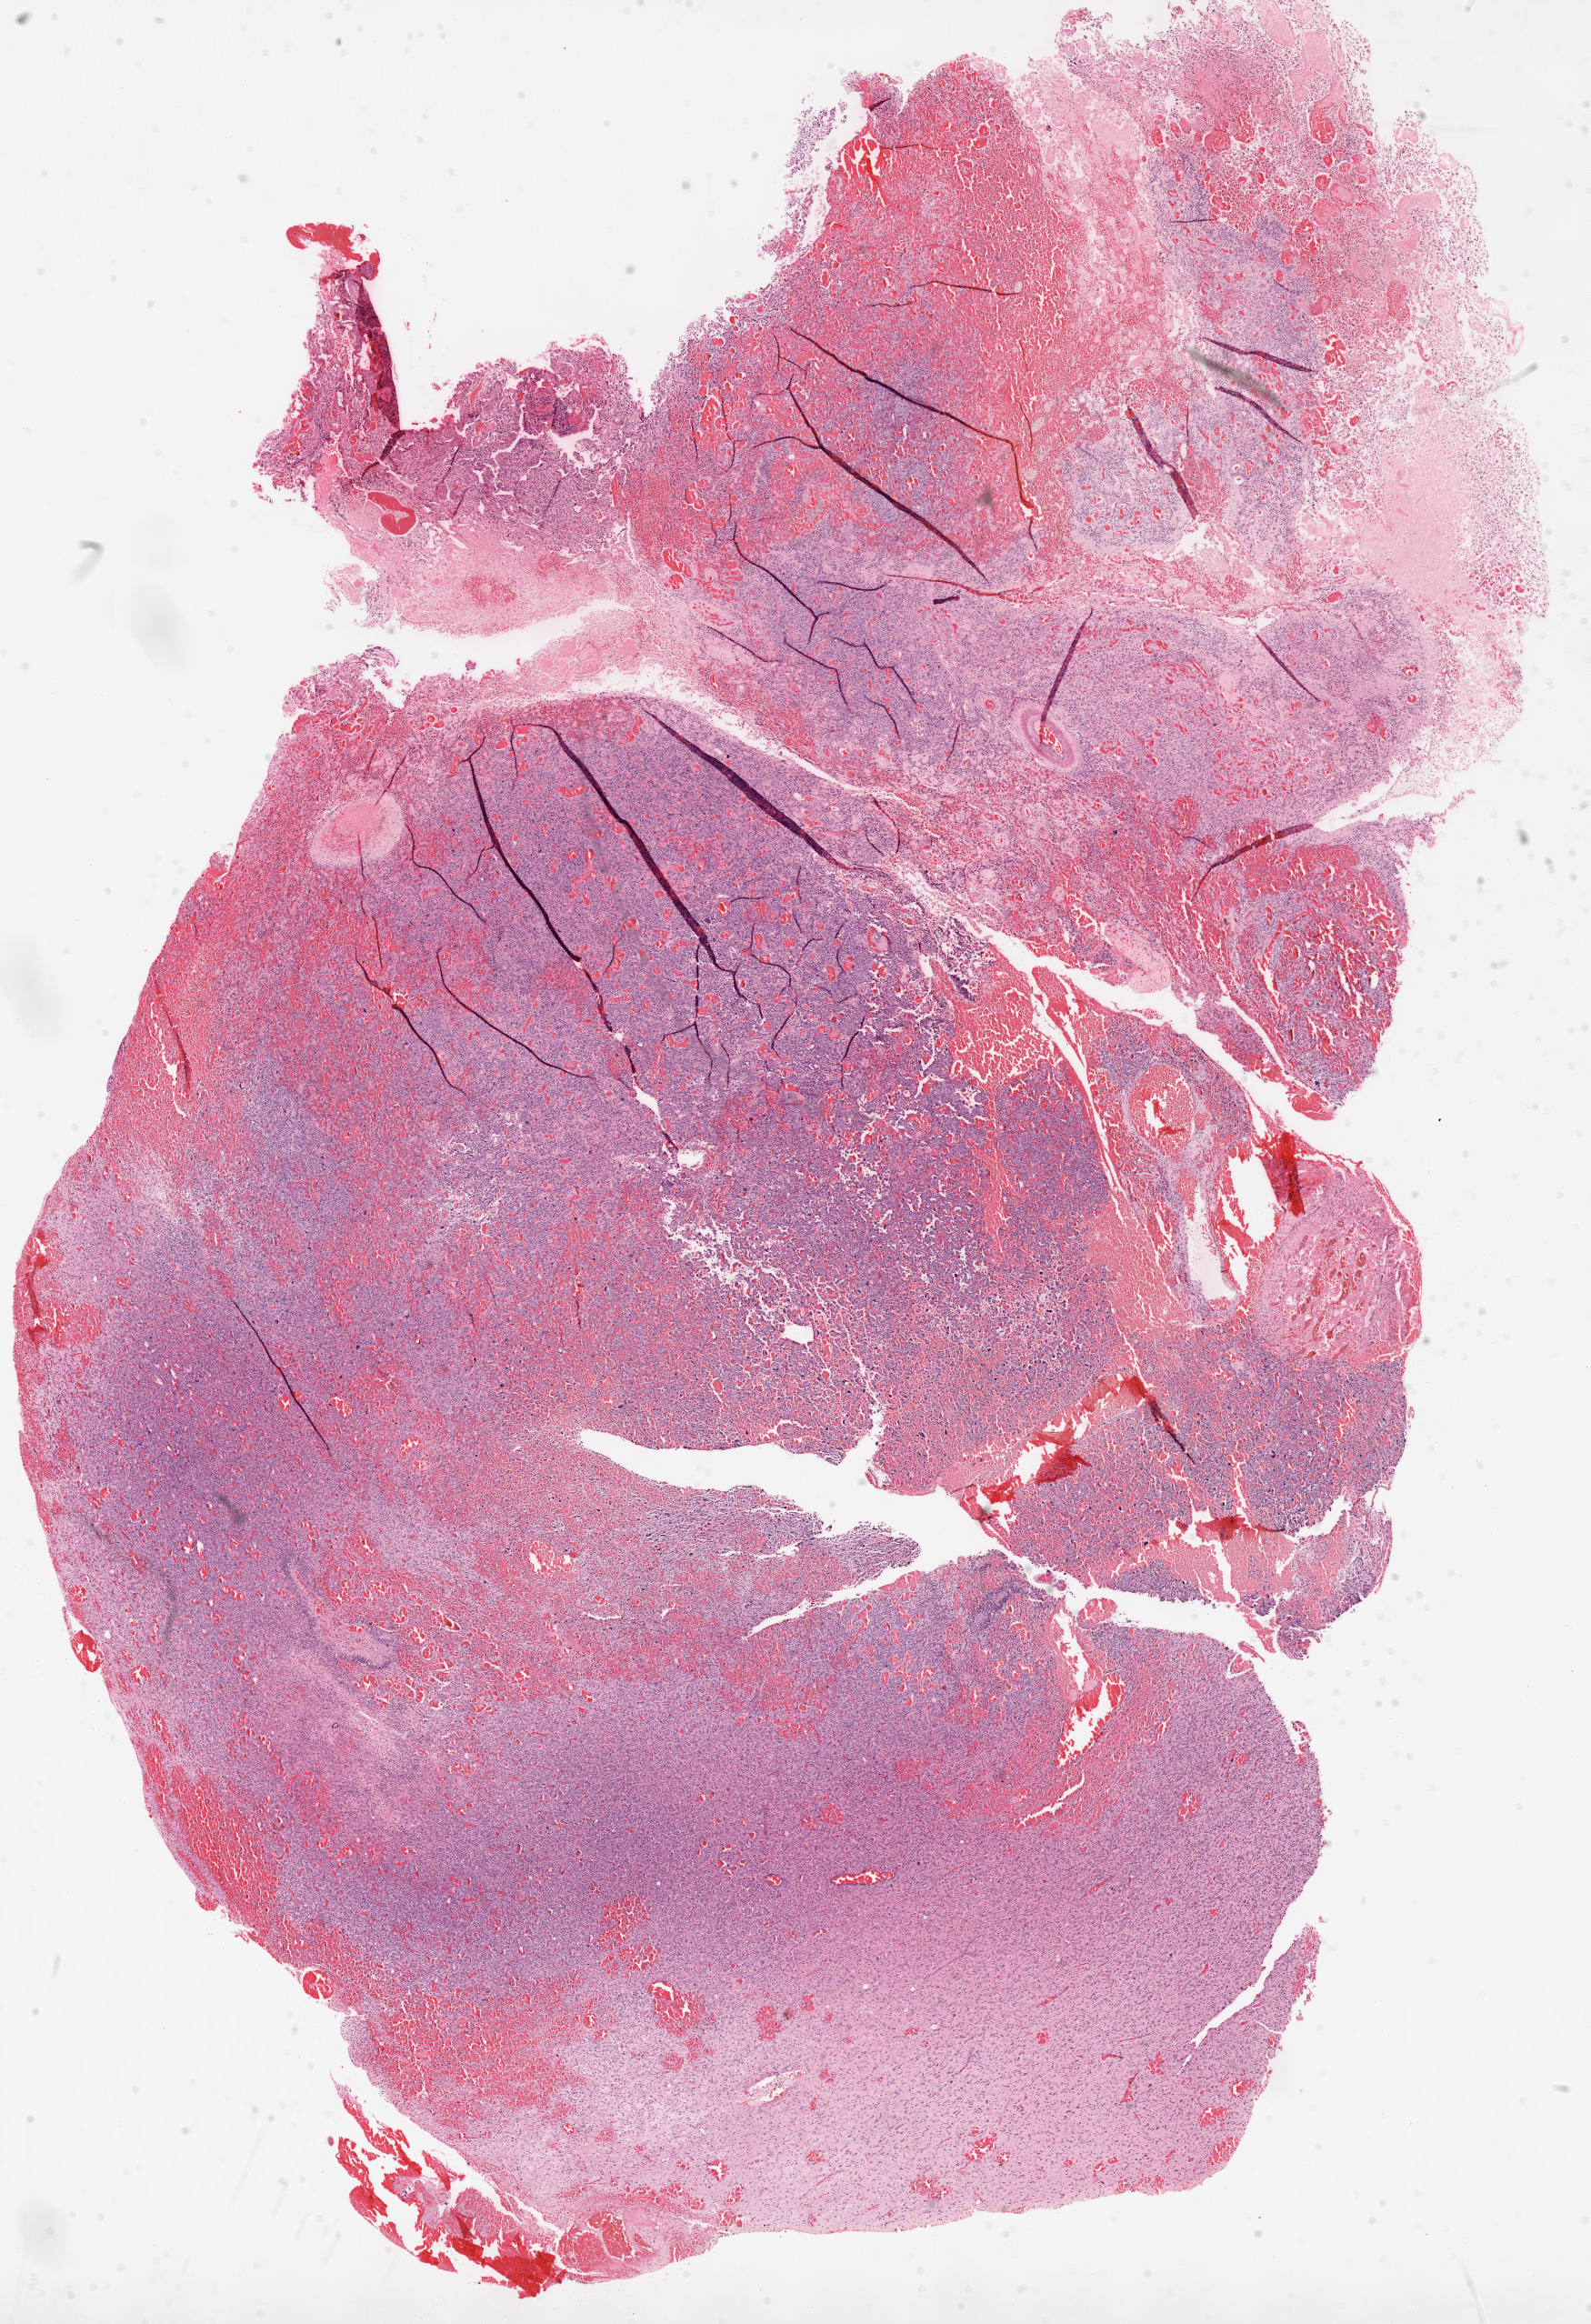
Digitized H&E-stained tissue section (whole slide) — a low-resolution overview of the entire scanned area, about 14.0 x 20.5 mm. FFPE section. Sample: primary tumour, brain. Patient: female, age at initial diagnosis 36 years.
Pathologic diagnosis: Glioblastoma.